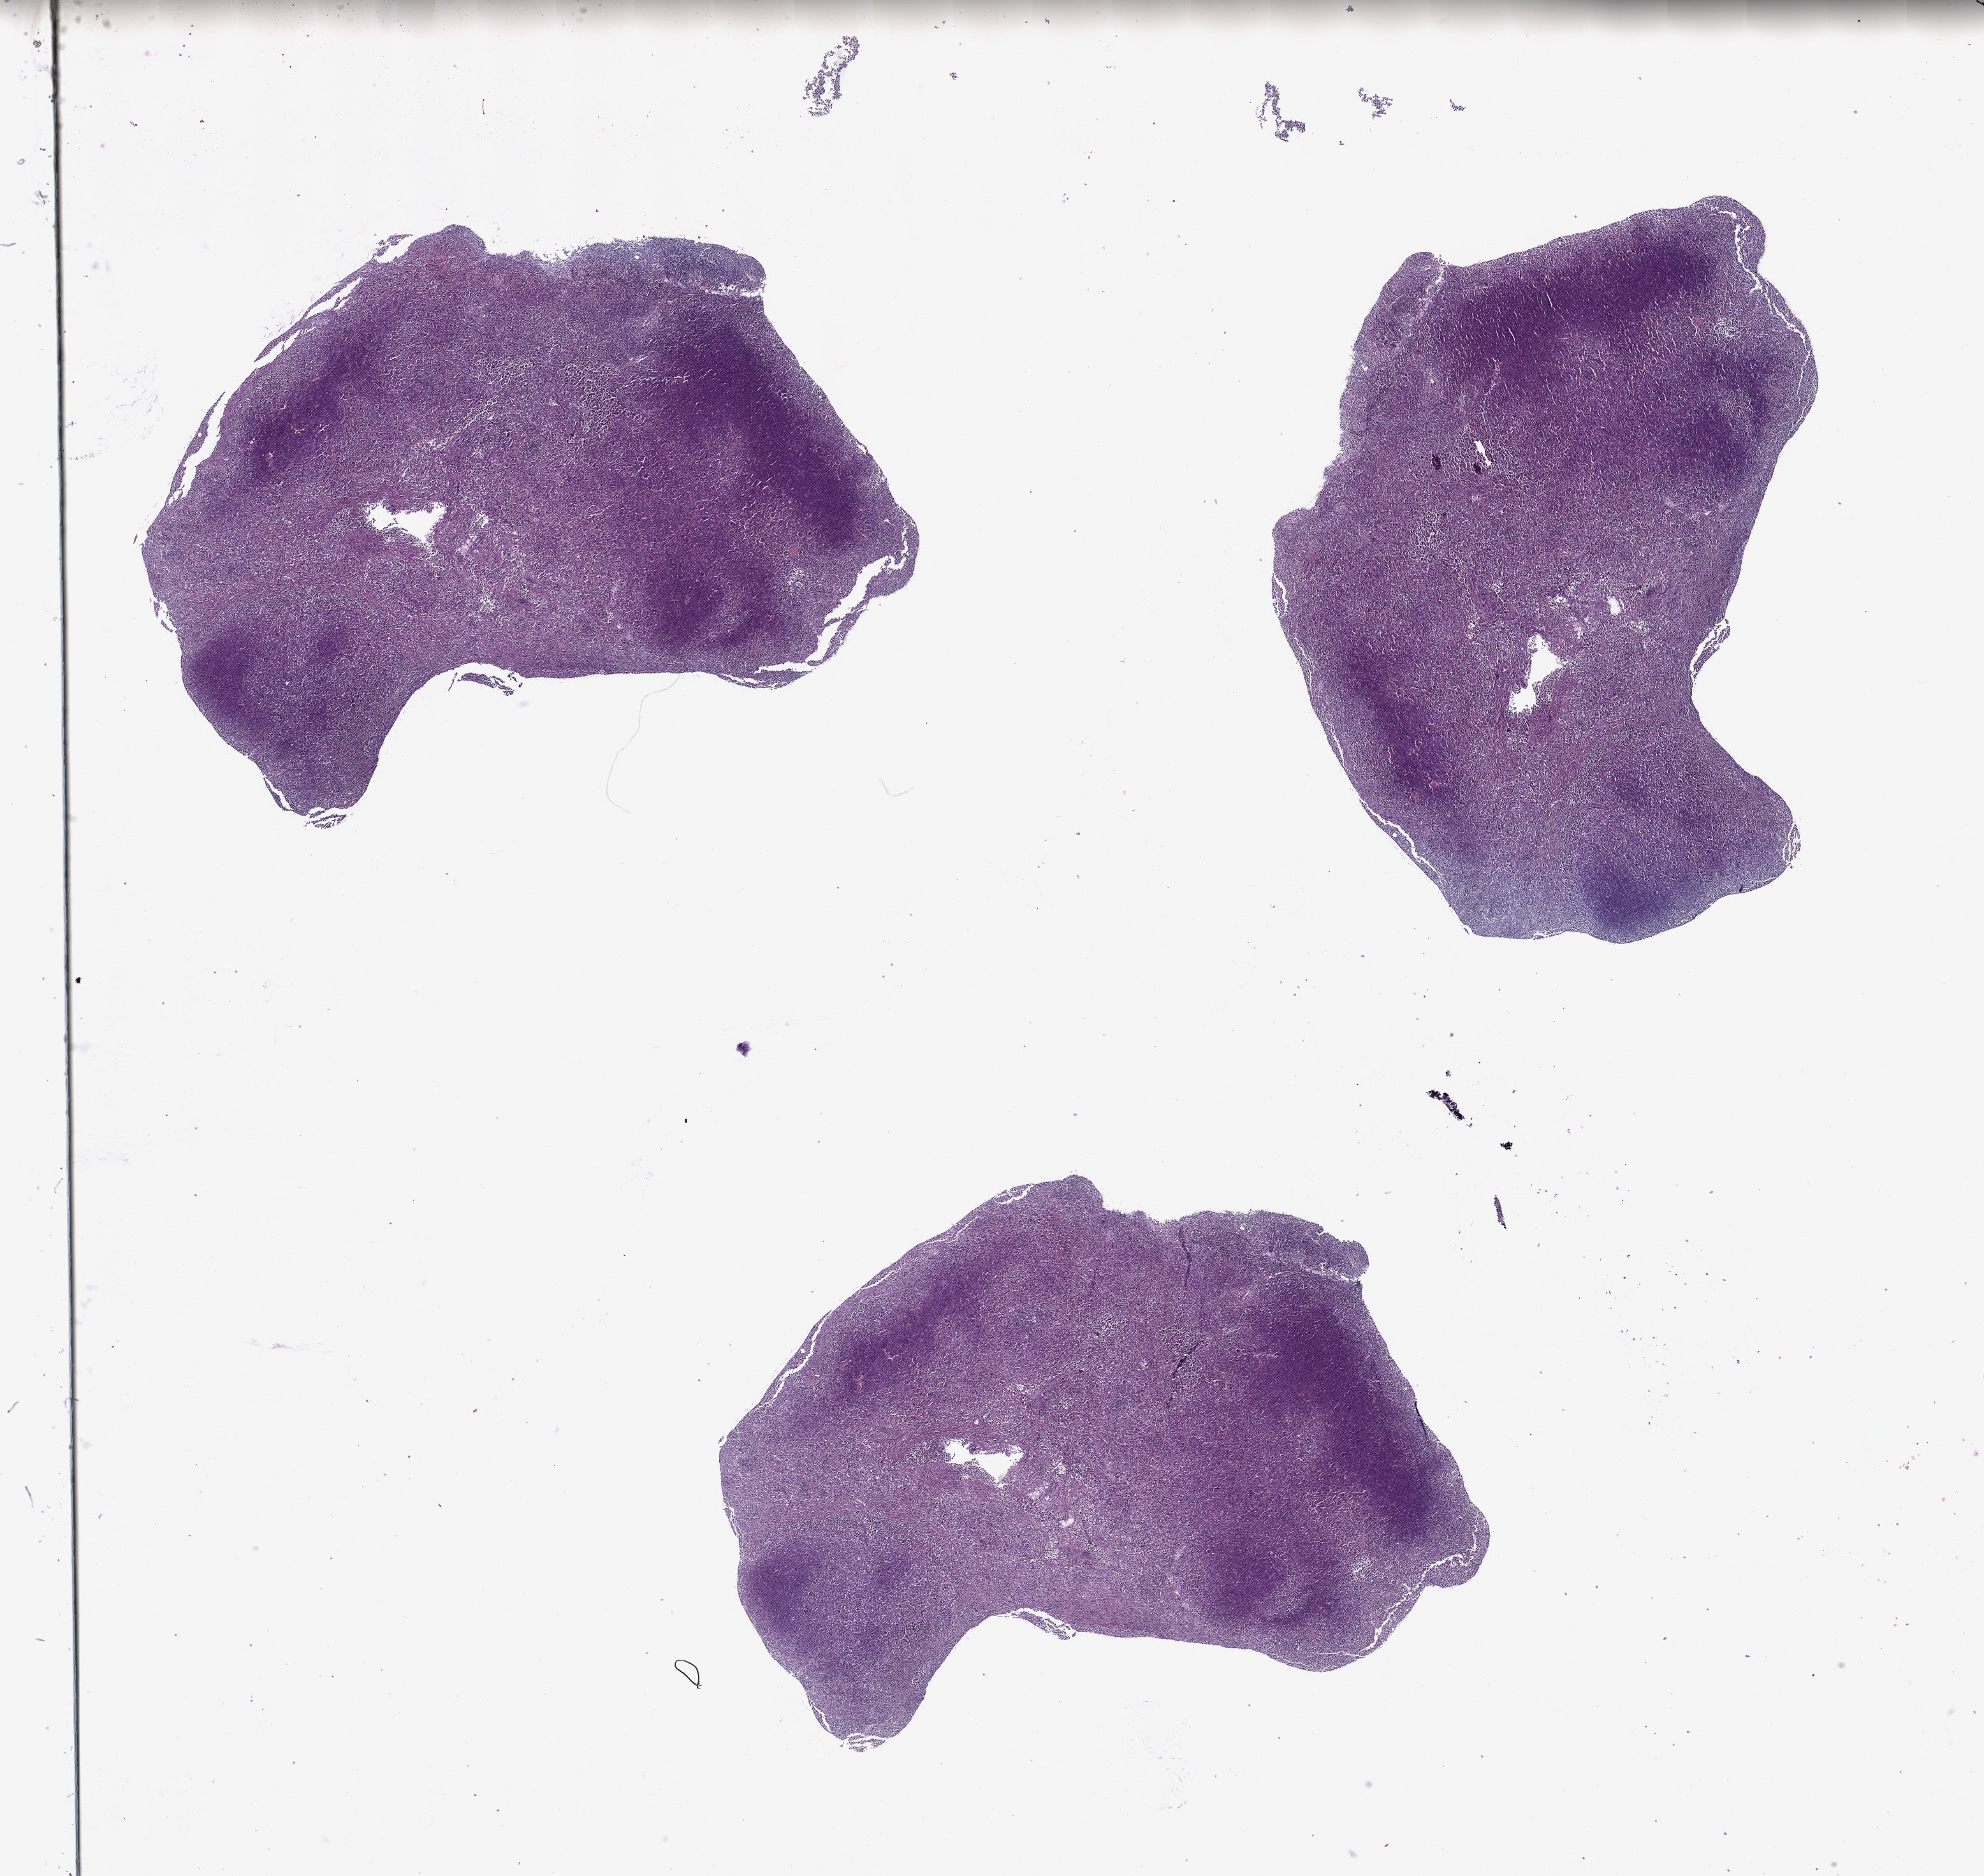
H&E whole-slide image, whole scanned area (about 24.6 x 23.3 mm) shown as a low-resolution overview; melanoma tumour tissue; sampled site not recorded. Female, 46 y/o.
AJCC pathologic stage: IIC. Primary tumour site (as recorded): extremities. Histologic diagnosis: Malignant melanoma, NOS.